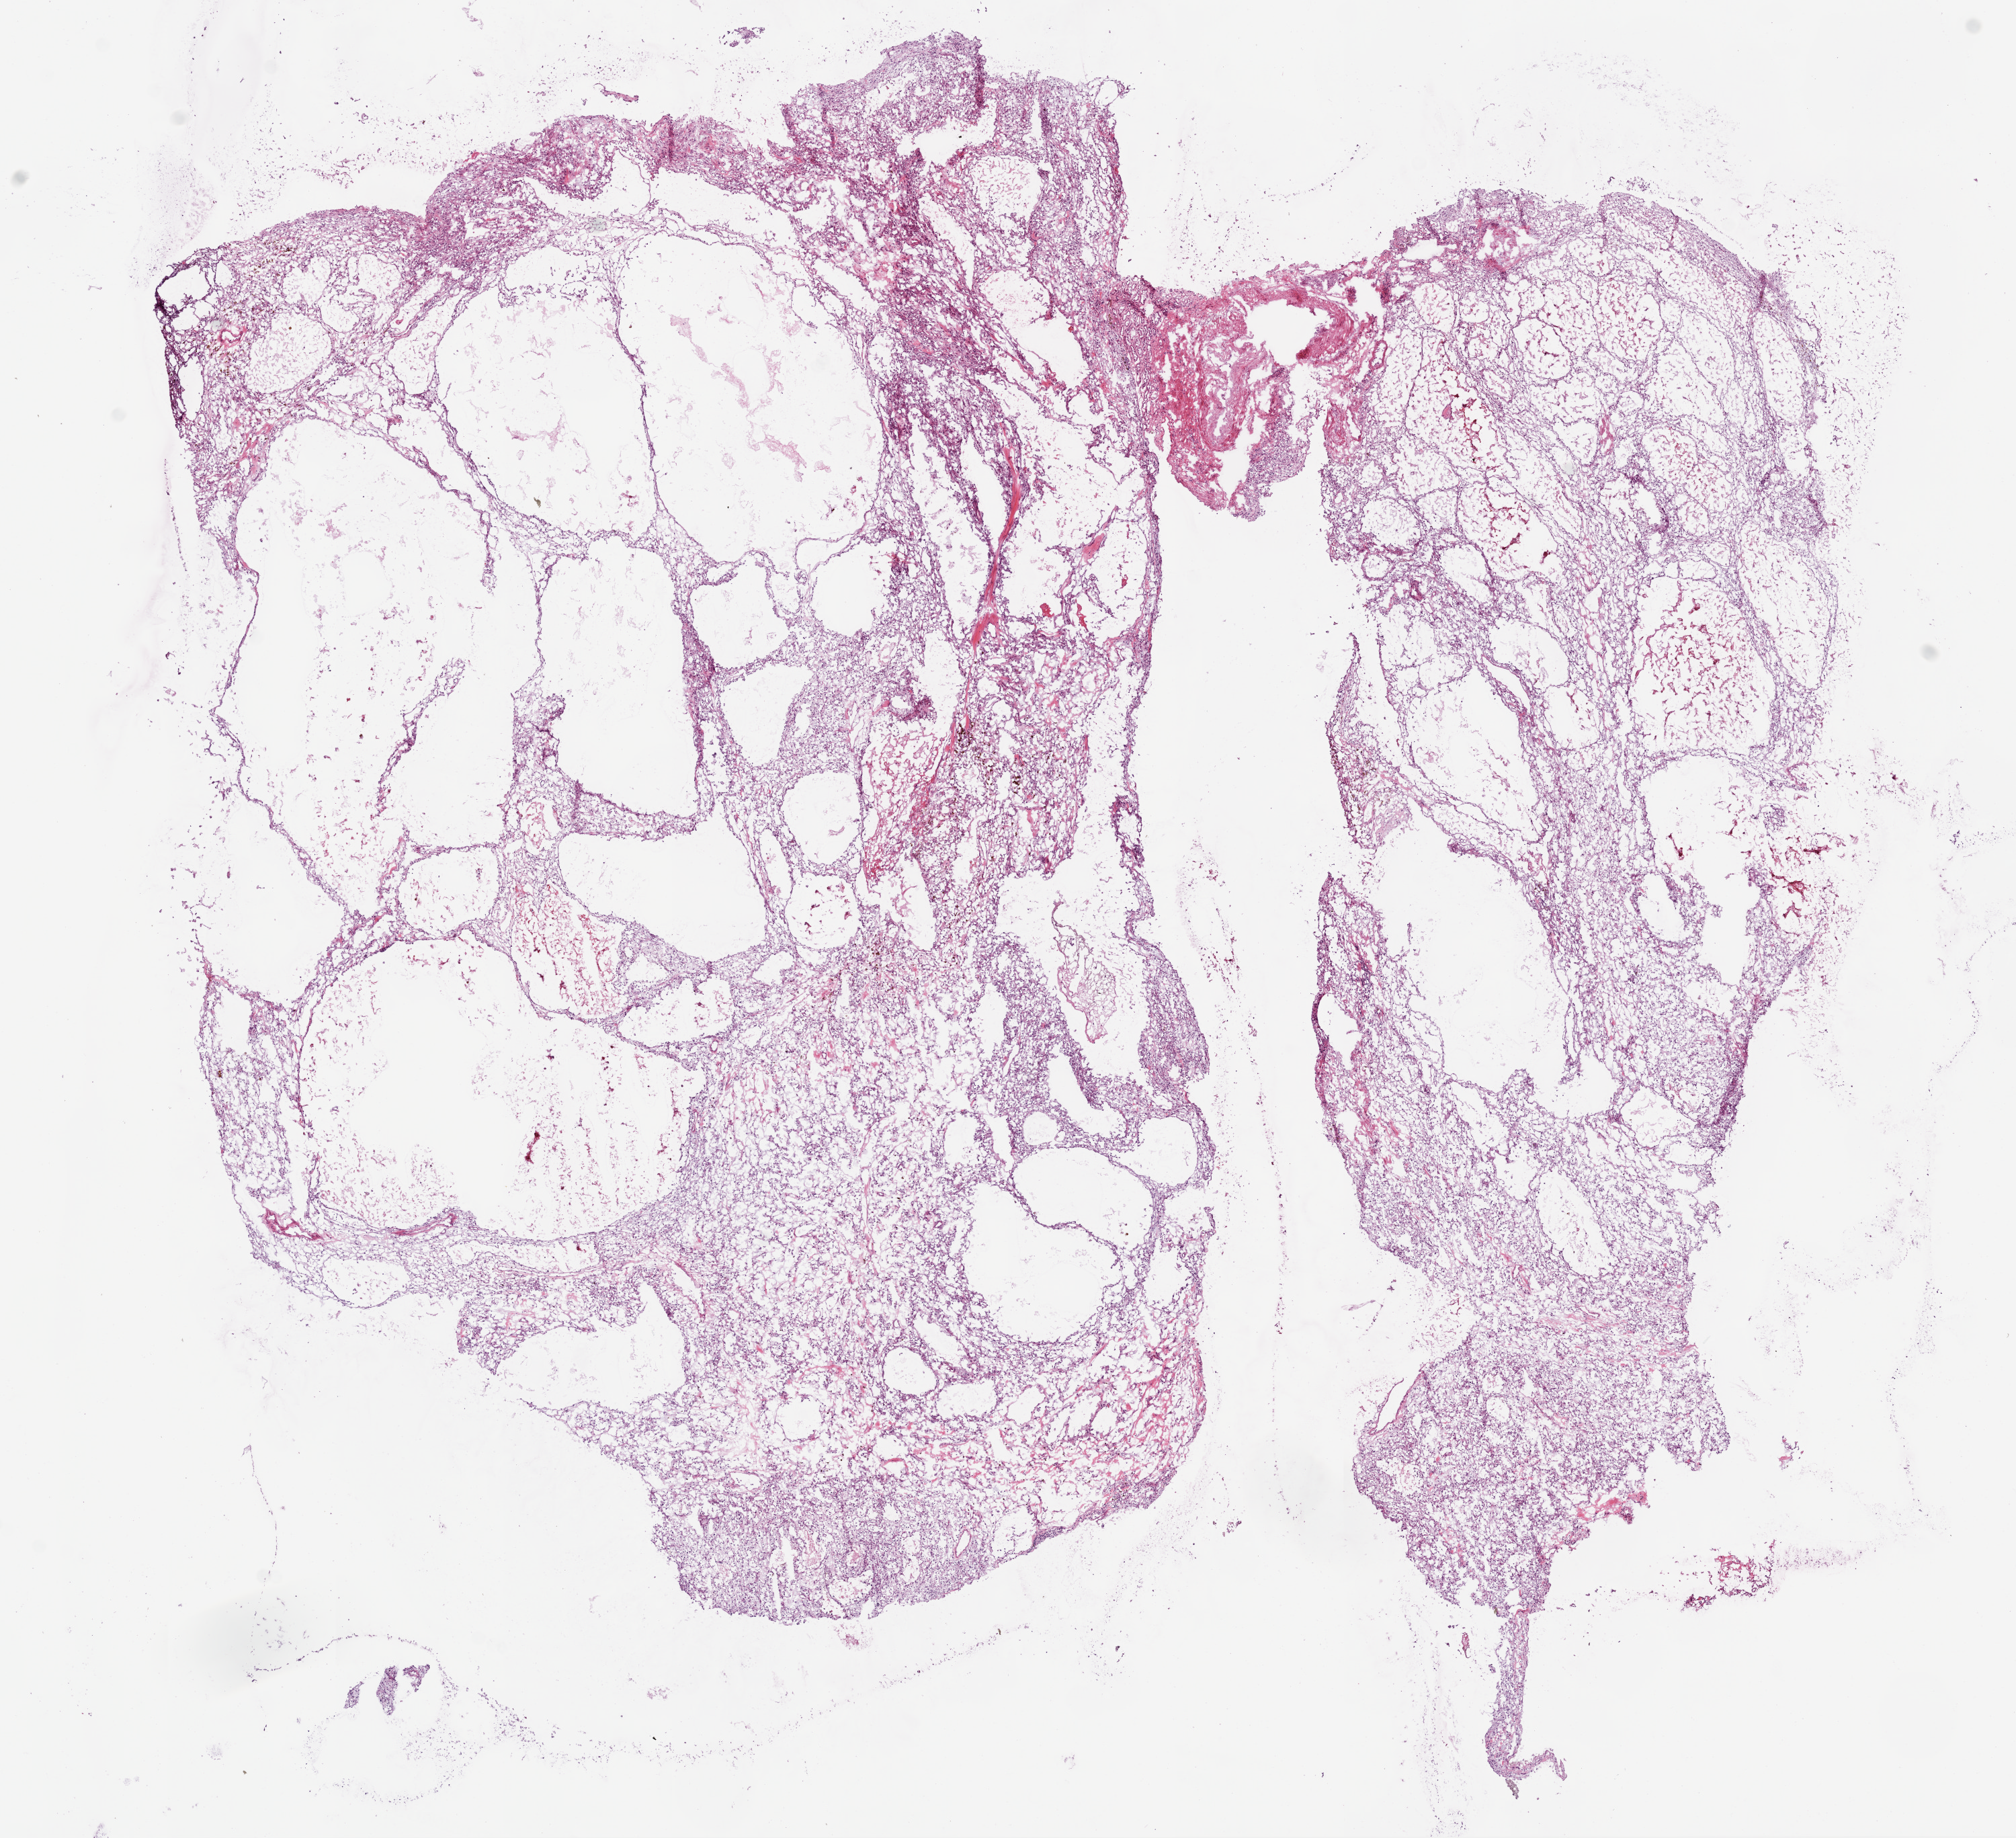
Digitized H&E tissue section (whole slide) — shown as a low-resolution overview of the whole scanned area (about 12.0 x 11.0 mm, slide scanned at 20x); frozen section from the bottom of the tissue portion; primary tumour sample from the kidney. Female, age 72 years at initial diagnosis. Histologic grade: G2 (moderately differentiated). Composition of this section per pathologist review: tumour cells 85%, tumour nuclei 80%, normal cells 0%, stromal cells 15%, necrosis 0%.
Histologic diagnosis: Clear cell adenocarcinoma, NOS. AJCC pathologic stage: I (7th edition).